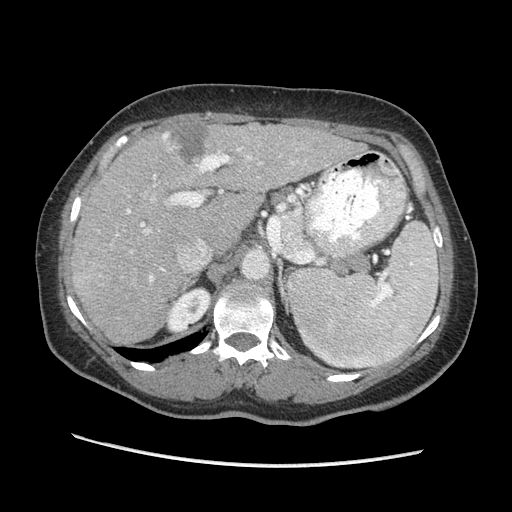
Contrast-enhanced abdominal CT (liver protocol), one axial slice; position 135 of 170 along the scan axis; reconstruction kernel STANDARD; soft-tissue window (W 400 / L 40 HU); 2.5 mm slice thickness; 512 × 512 image matrix. From the clinical record (not read from this slice): diagnosis: hepatocellular carcinoma (patient treated with transarterial chemoembolisation; whether this scan precedes or follows treatment is not stated here); TNM stage (as recorded): Stage-II; Child-Pugh class: A; tumour differentiation: no biopsy; tumour size: 4 cm.
Annotated regions visible in this slice (semi-automatic segmentation, software-assisted and operator-edited):
- liver parenchyma outside the tumour (the mass and vessels are separate outlines, so this box may not span the whole liver): bounding box [x1, y1, x2, y2] px = [70, 122, 366, 344]
- mass: [161, 124, 206, 163]
- liver vessels: [127, 147, 294, 281]